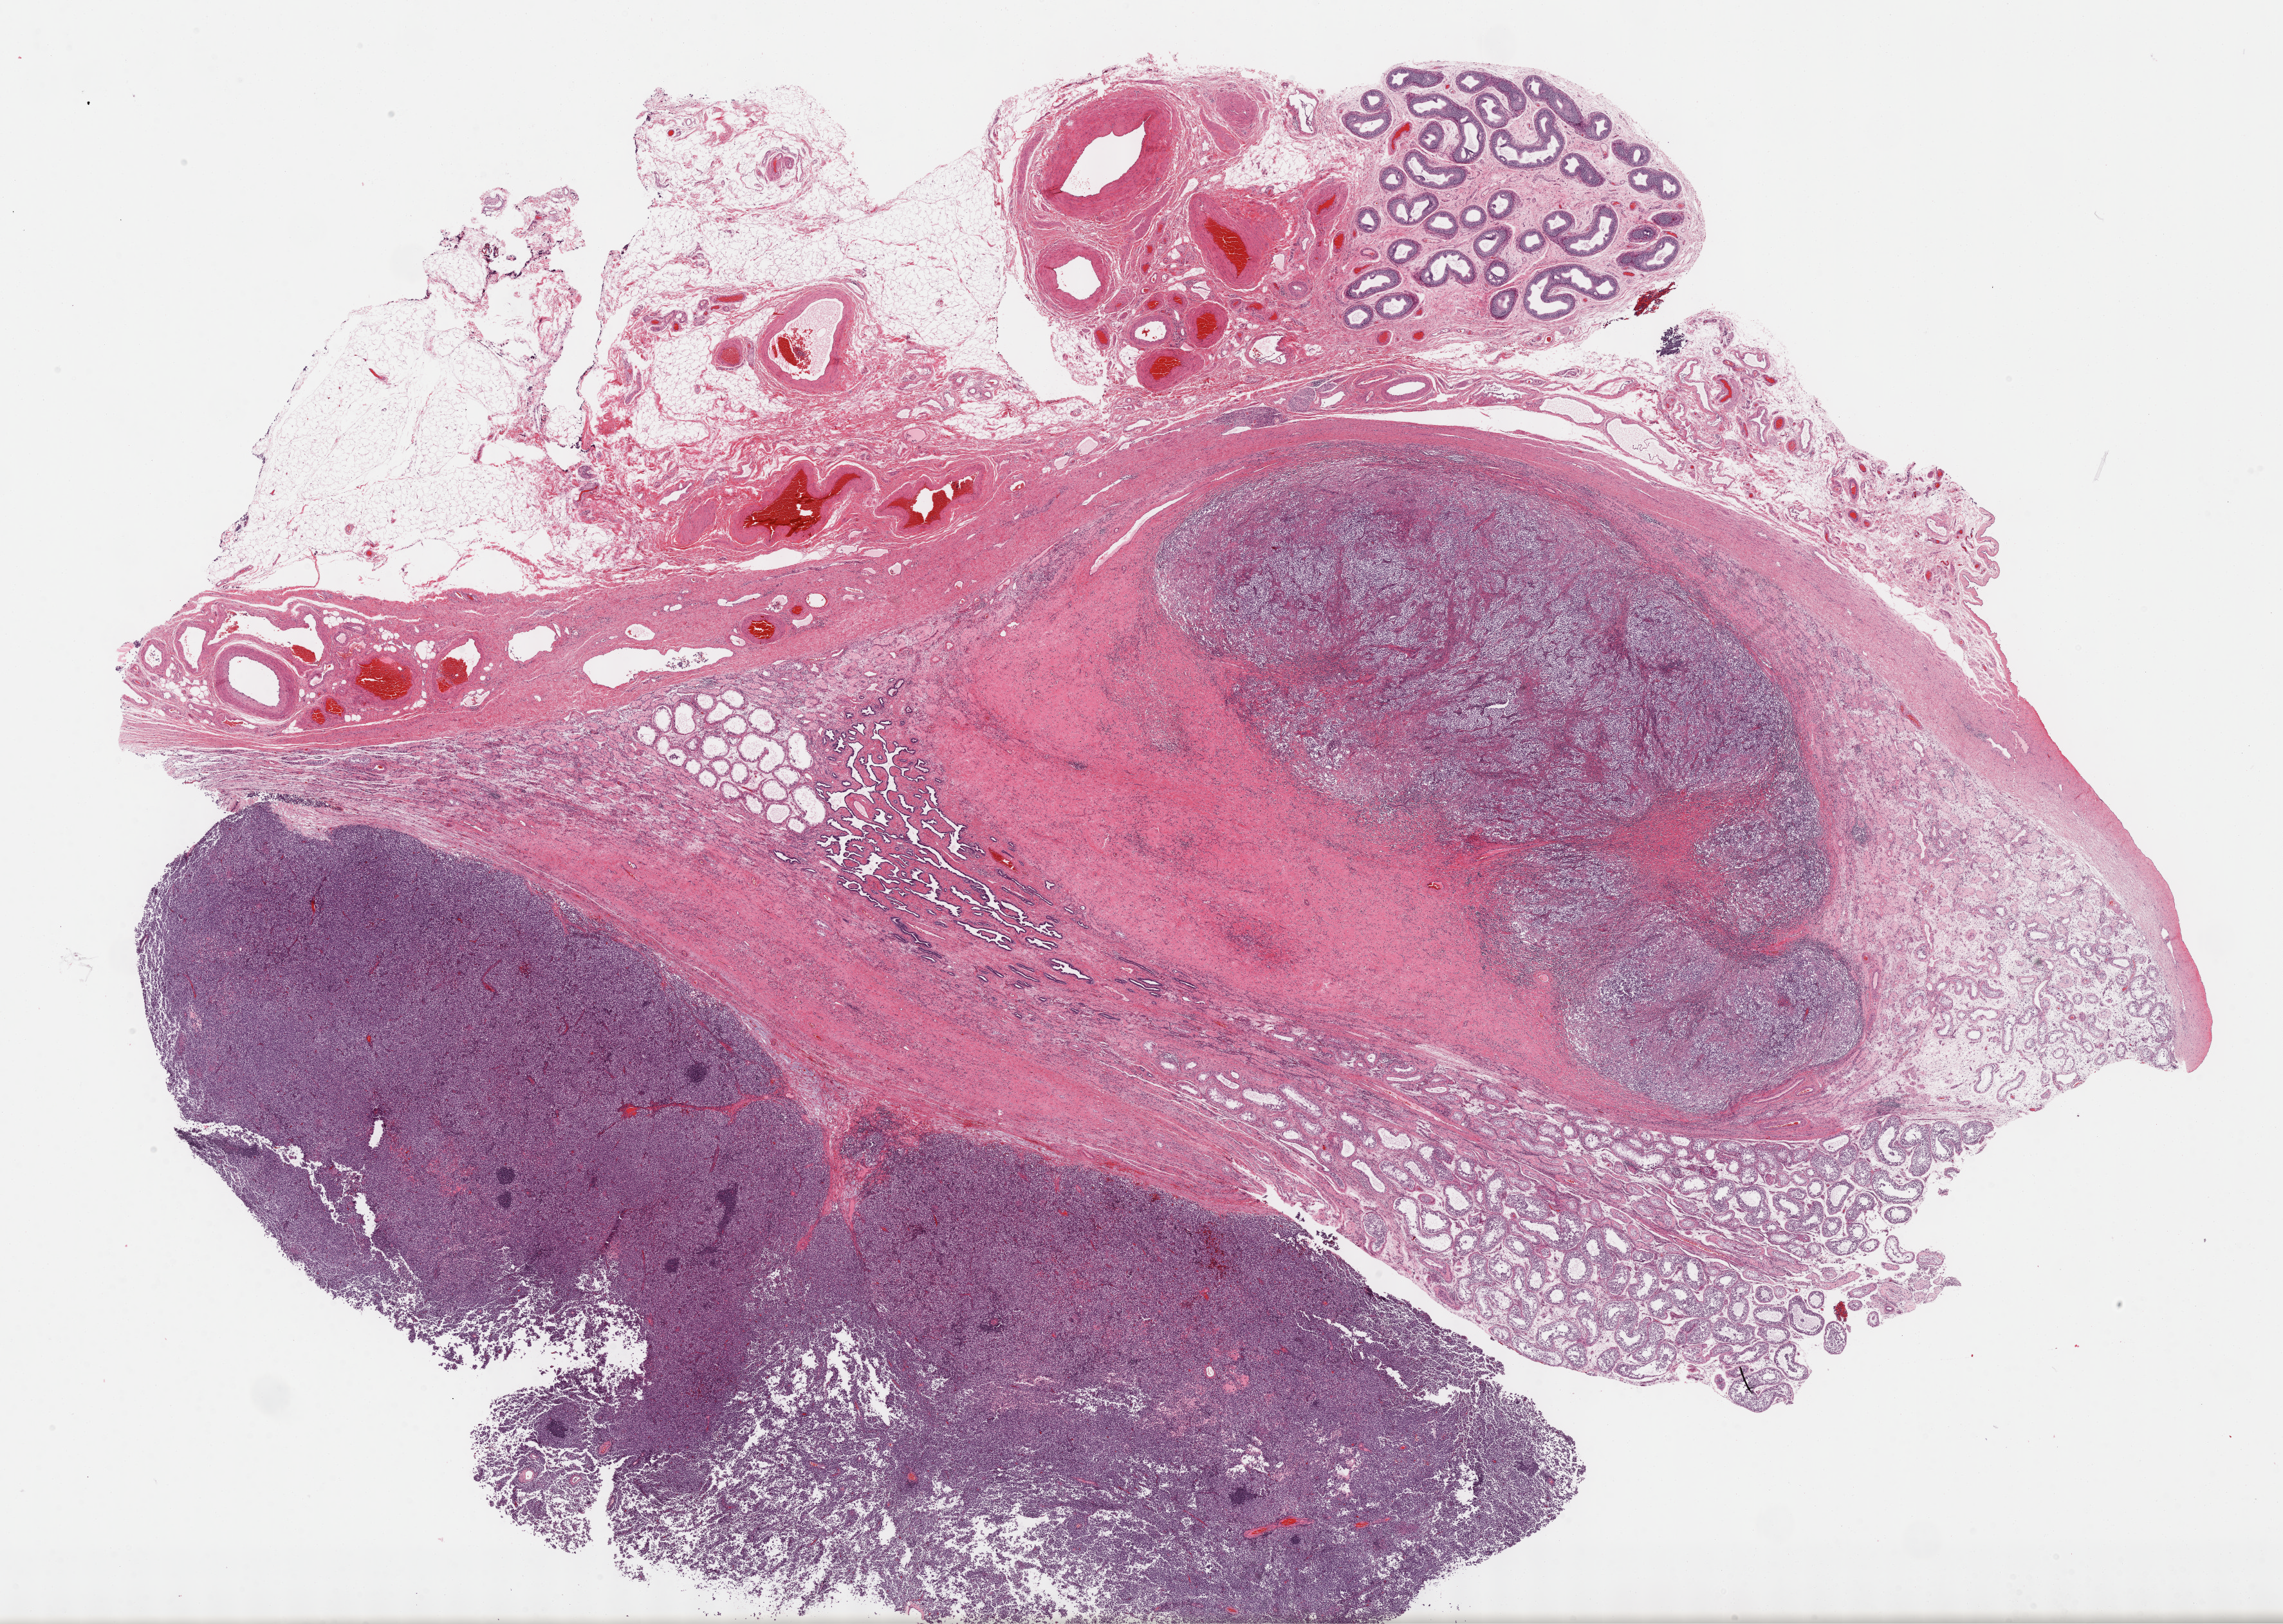
Digitized H&E tissue section (whole slide), a low-resolution overview of the entire scanned area, about 28.7 x 20.4 mm (slide scanned at 40x); formalin-fixed paraffin-embedded (FFPE) diagnostic section; primary tumour sample from the testis. Male patient; age at initial diagnosis 37 years.
• AJCC pathologic stage: IS (7th edition)
• pathologic diagnosis: Seminoma, NOS
• laterality: left